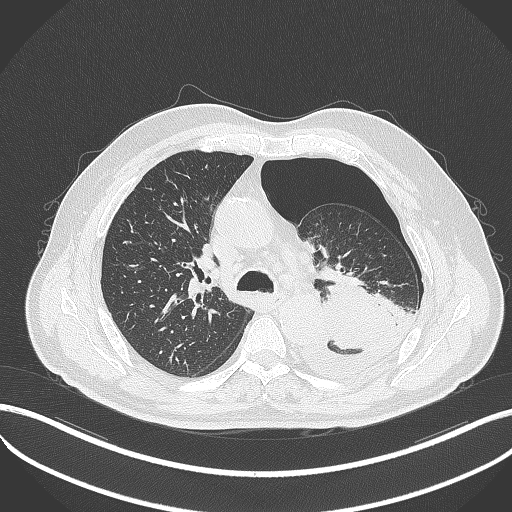
Chest CT, one axial slice; slice 342 of 464 in the series (ordered by position); 120 kVp; lung window (W 1500 / L -600 HU); 1 mm slice thickness; 512 × 512 image matrix, field of view 400 × 400 mm. Male patient, age 76 years. Case-level facts recorded for this patient, not image findings: clinical TNM (as recorded): T3 N0 M1b.
Annotated regions visible in this slice (bounding box drawn by a radiologist):
- lung tumour (recorded histology: adenocarcinoma): bounding box [x1, y1, x2, y2] px = [322, 270, 399, 353]